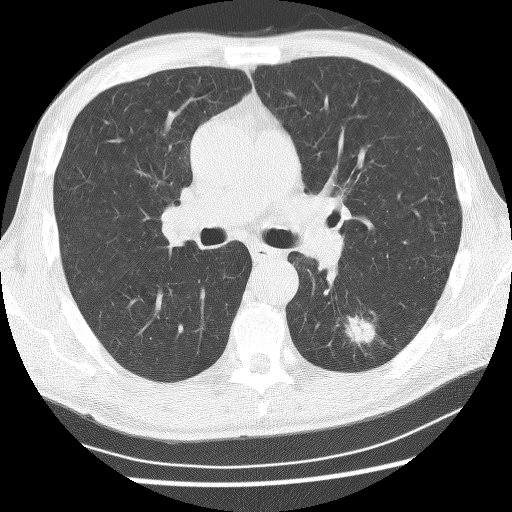
Chest CT (low-dose screening protocol), one axial image. Baseline screening round. Lung window (W 1500 / L -600 HU). 2.5 mm slice thickness. Slice 105 of 253 in the series. Male participant, aged 62 years at enrolment. Current smoker at enrolment.
- Expert-annotated lung lesion, bounding box [x1, y1, x2, y2] px = [331, 308, 381, 353].
- Screening reader's record for this exam (one nodule recorded; not confirmed to be the boxed lesion): non-calcified nodule or mass ≥4 mm, left lower lobe, 21 × 17 mm, spiculated (stellate) margins, soft tissue attenuation.